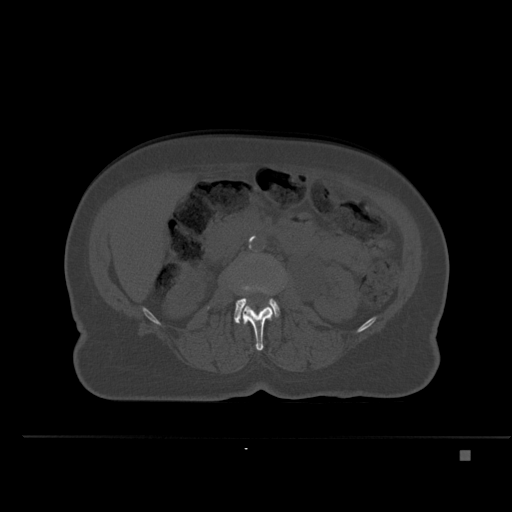
CT including the spine, one axial slice. Position 209 of 477 along the scan axis. Bone window (W 1800 / L 400 HU). 512 × 512 image matrix, field of view 422 × 422 mm. Patient: female, 74 years. From the clinical record (not read from this slice): primary cancer: colon.
Outlined on this slice (semi-automatically segmented with operator editing):
- L2 vertebra: bounding box [x1, y1, x2, y2] px = [242, 276, 284, 351]
- L3 vertebra: [234, 284, 280, 324]